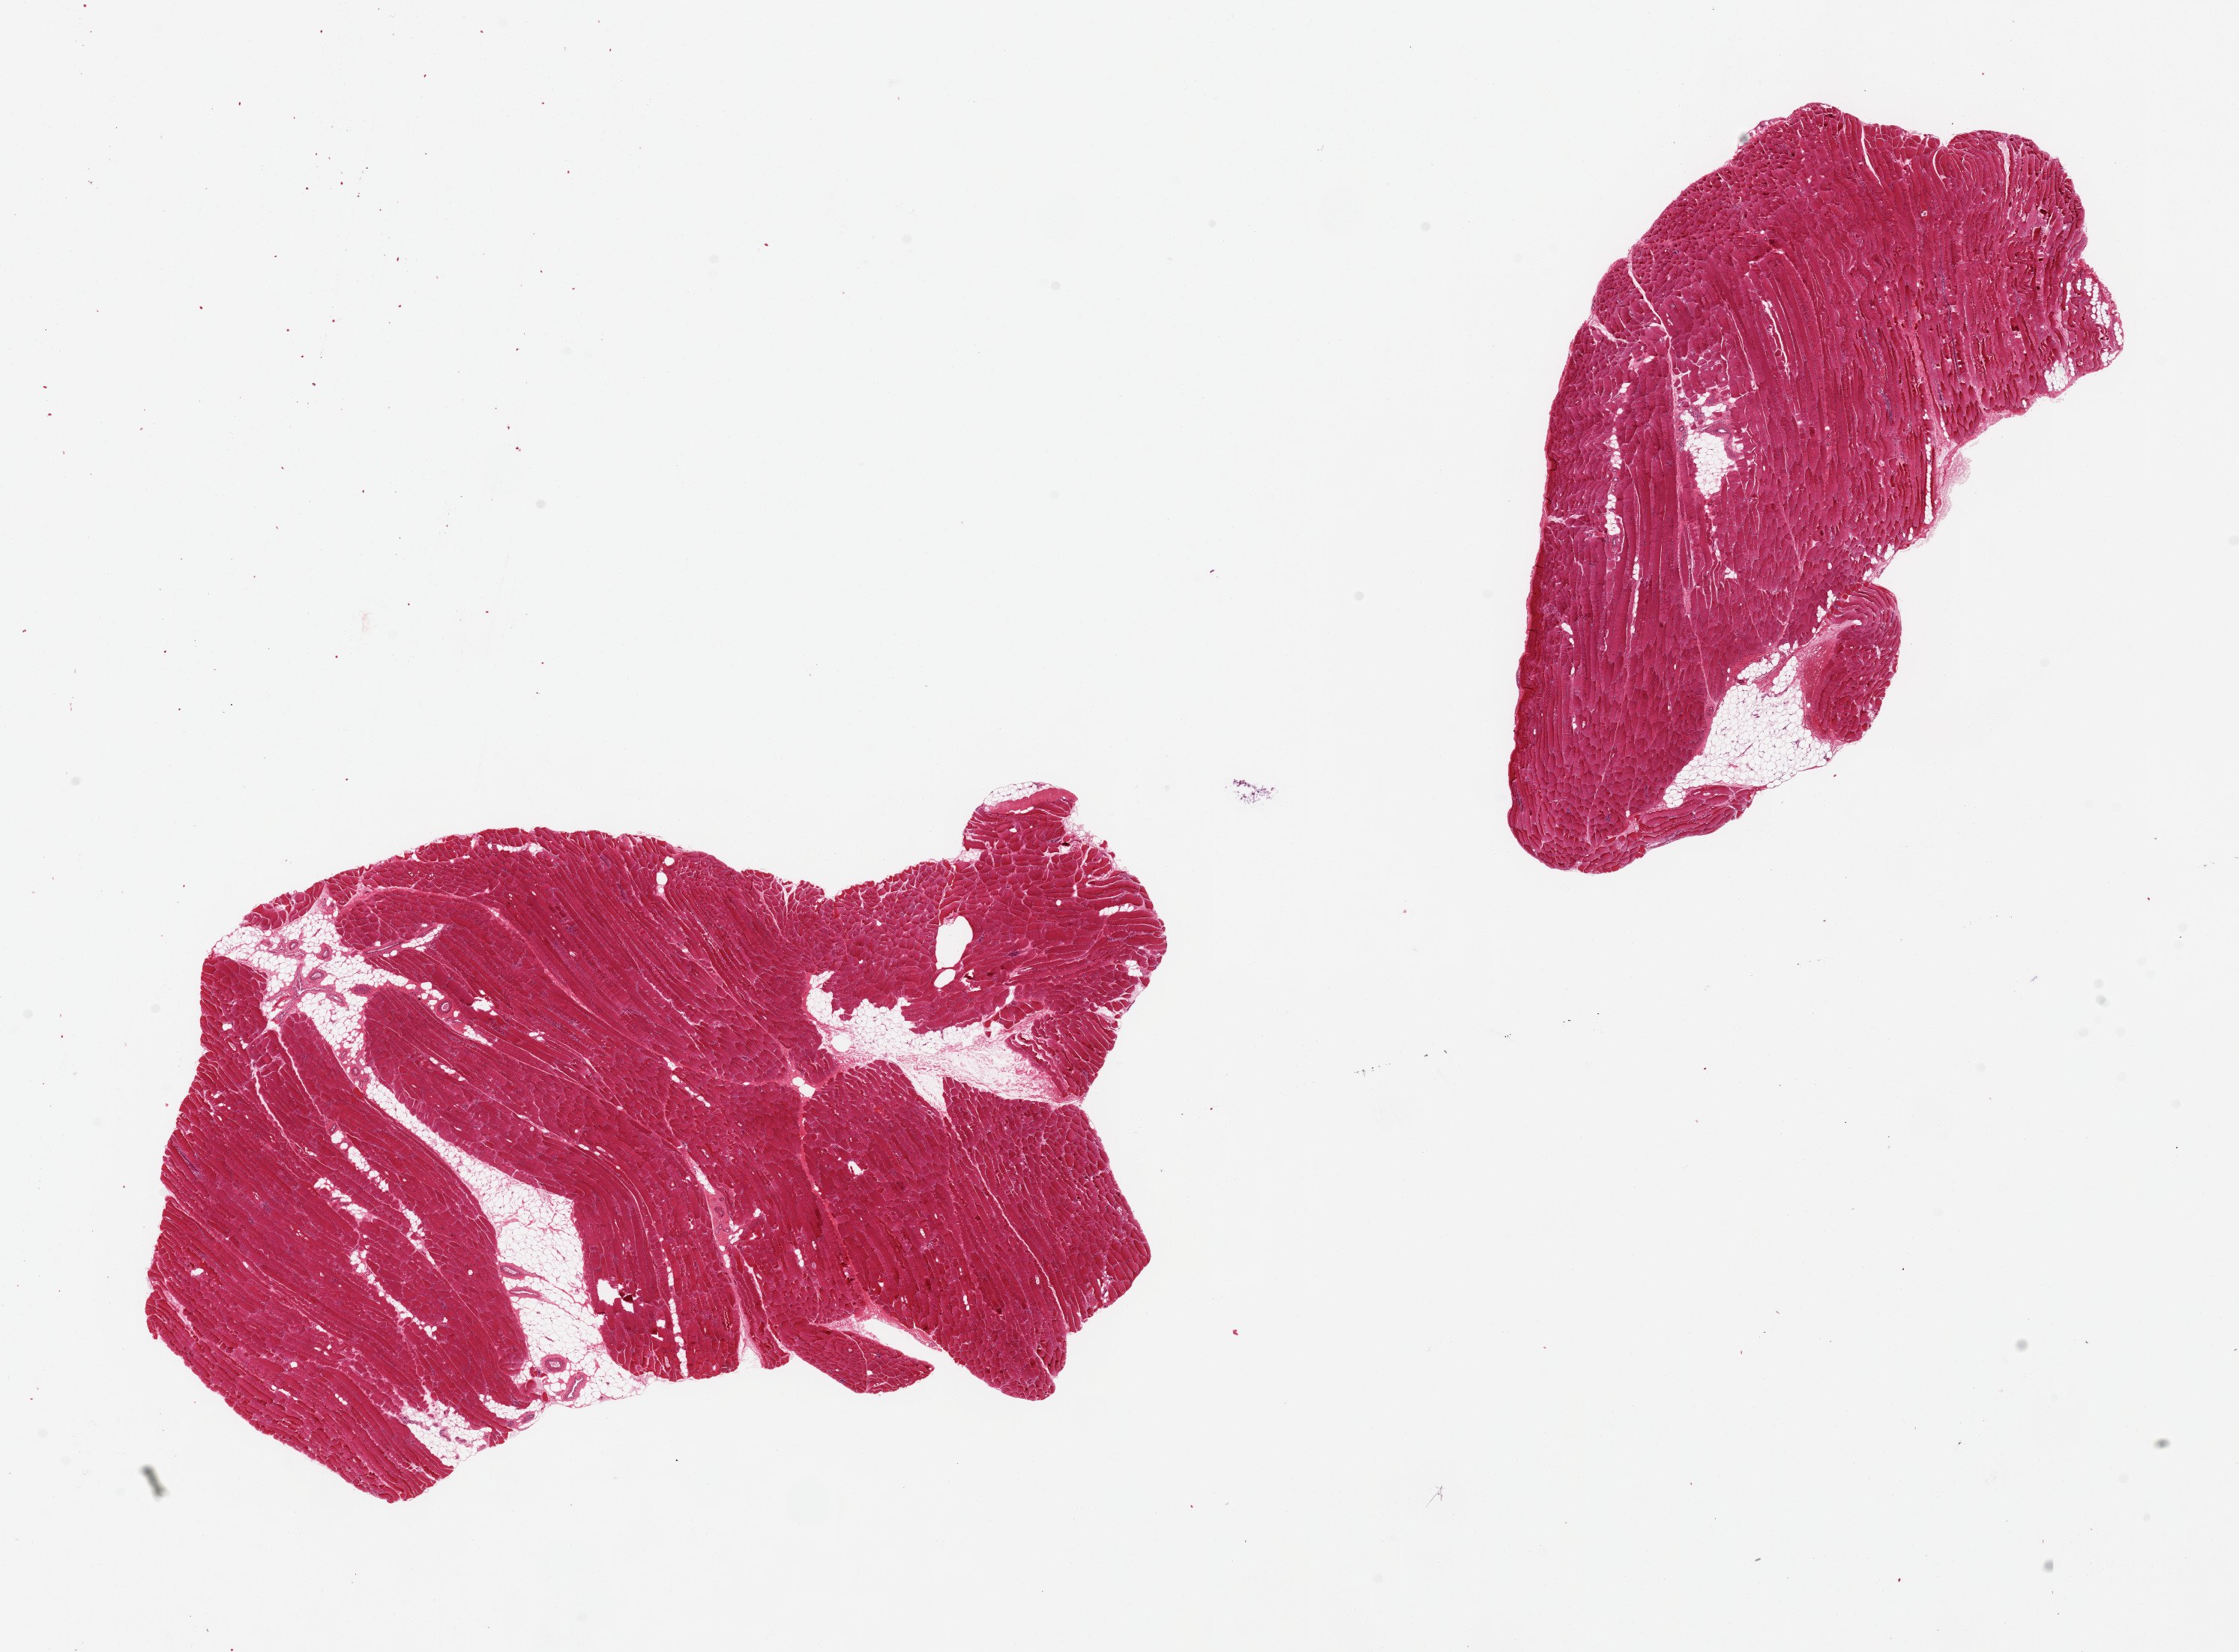
Whole-slide image, hematoxylin and eosin (H&E) stain — shown as a low-resolution overview of the whole scanned area (about 23.6 x 17.4 mm, acquisition: 20x scan), PAXgene-fixed paraffin-embedded (PFPE) section, section of skeletal muscle (target tissue), tissue donor sample.
Reviewer comment on this tissue sample: 2 pieces ~10x6mm, ~5-10% interstital fat.